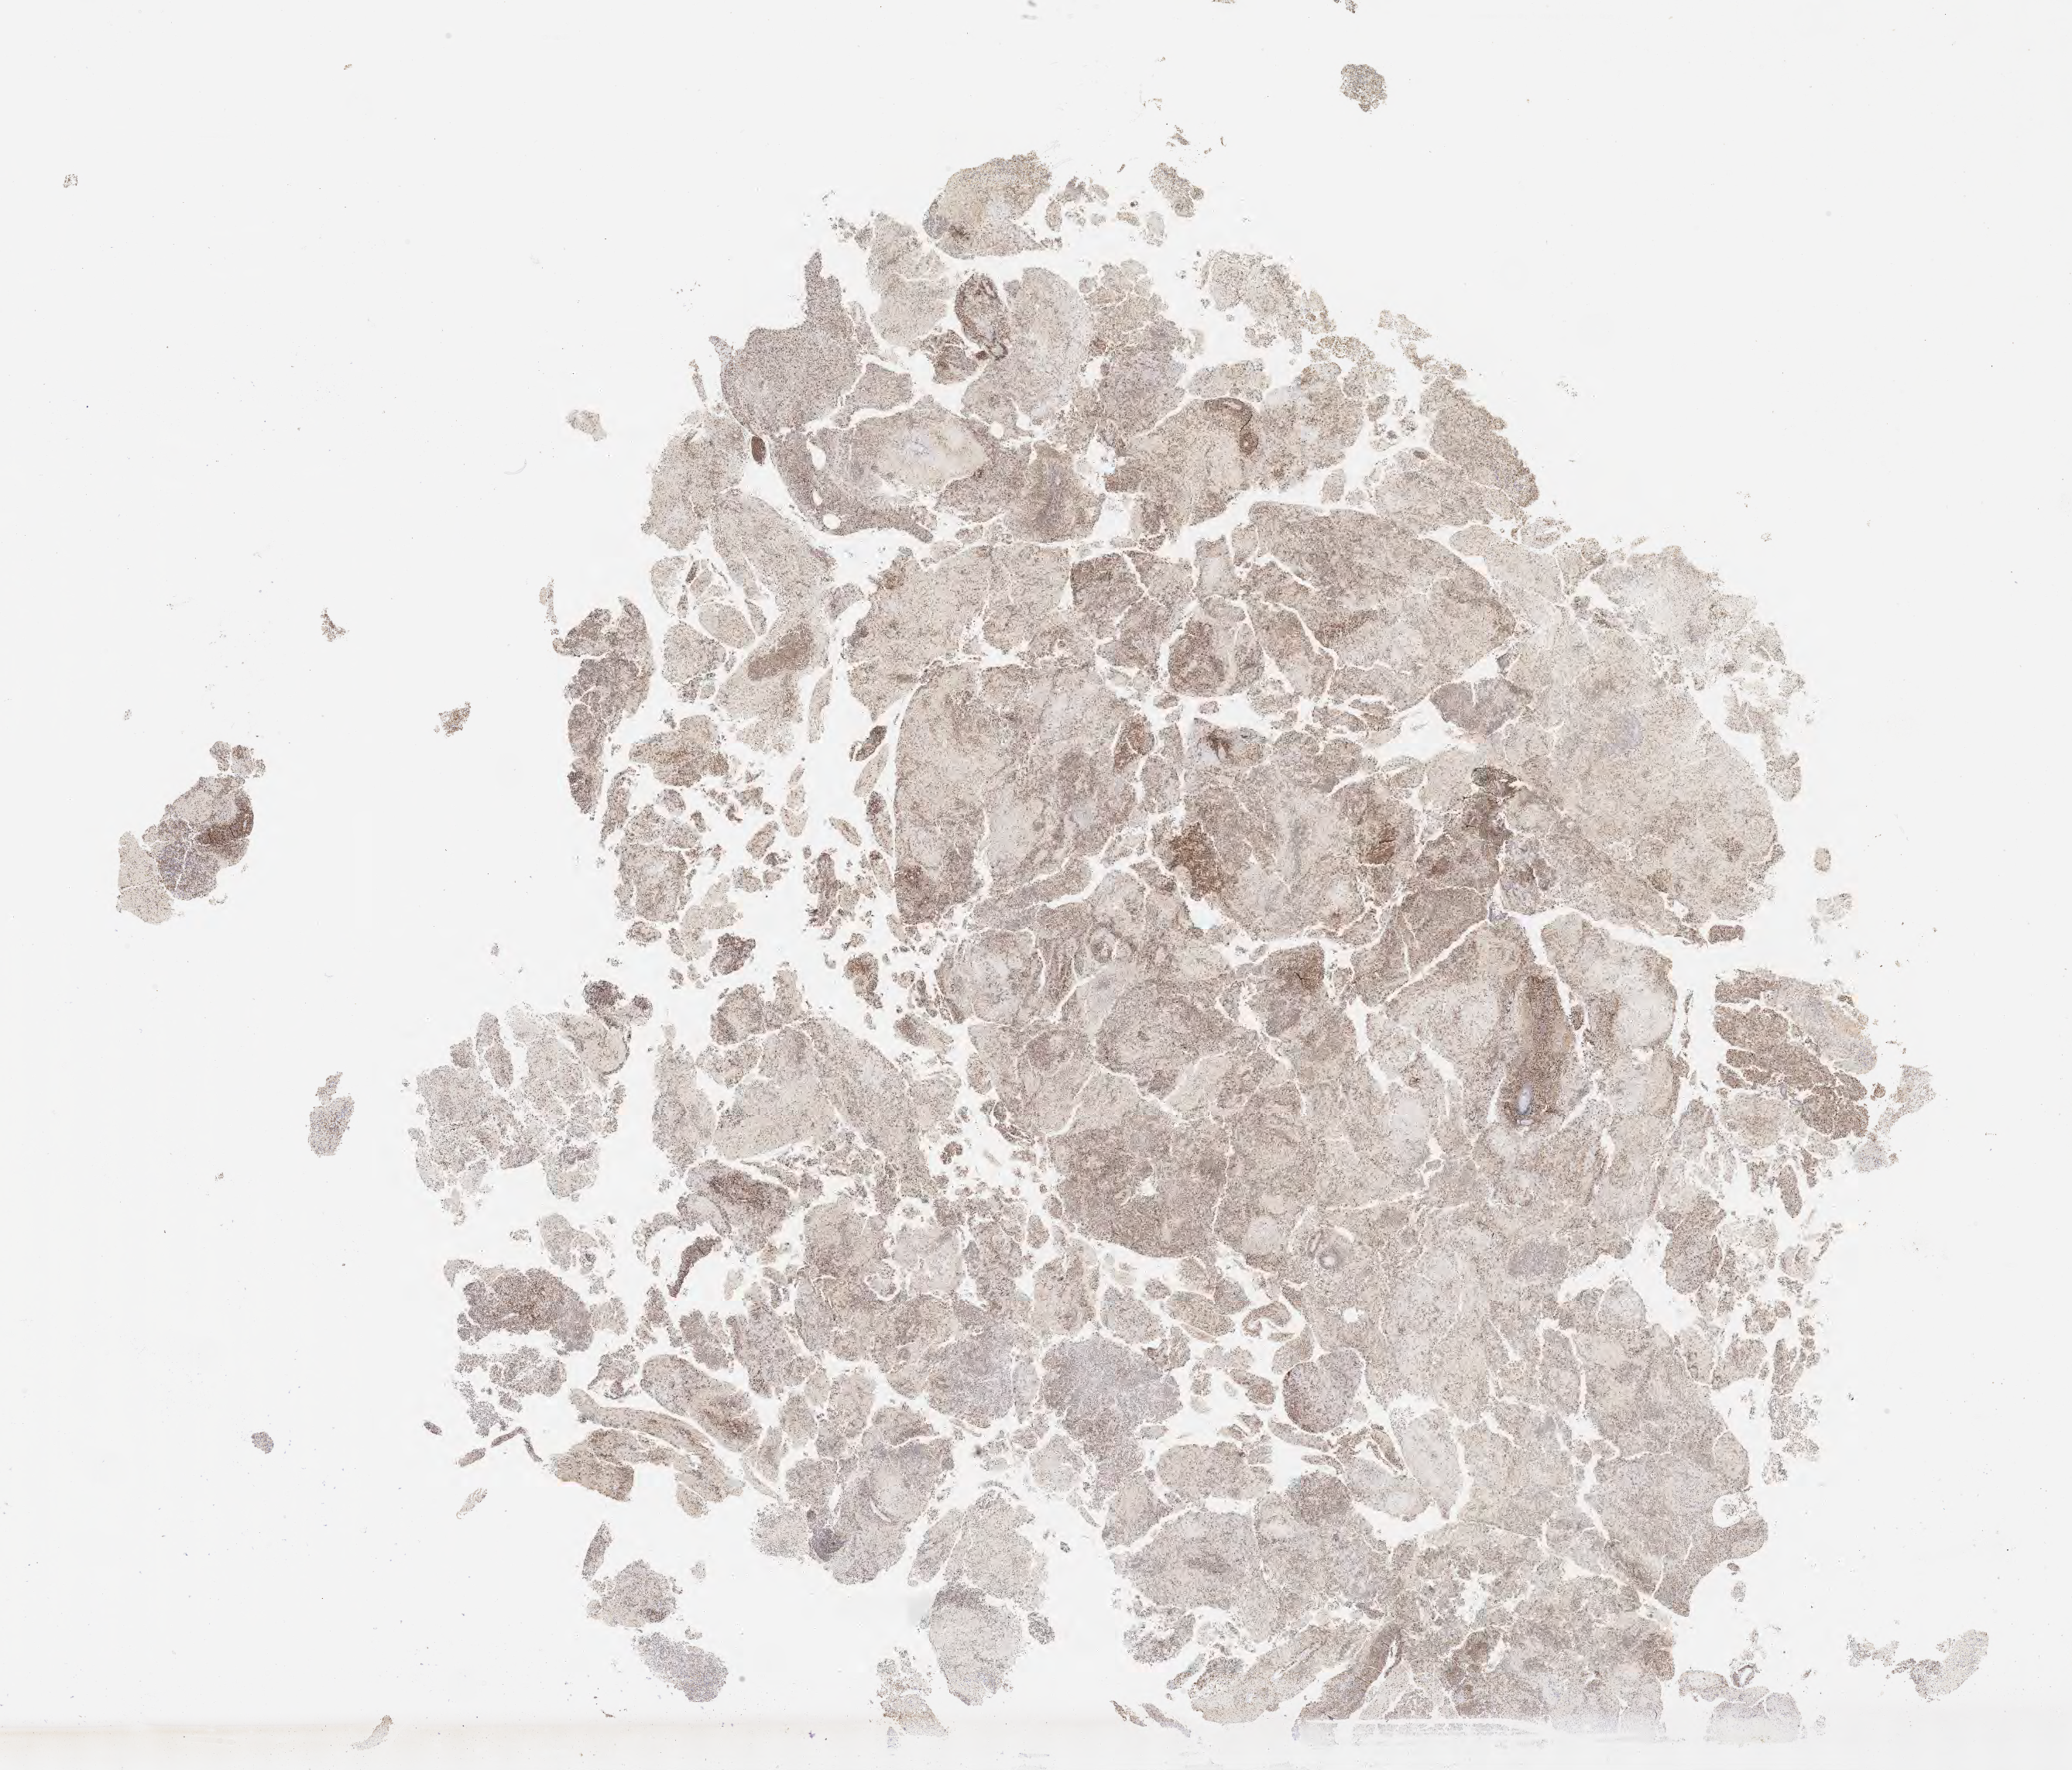
IHC for CD79a, whole-slide image — whole scanned area (about 21.6 x 18.5 mm) shown as a low-resolution overview. Specimen: tumor tissue. Anatomic site: brain. Male patient, age 51 years.
Diagnosis: Diffuse large B-cell lymphoma, NOS.